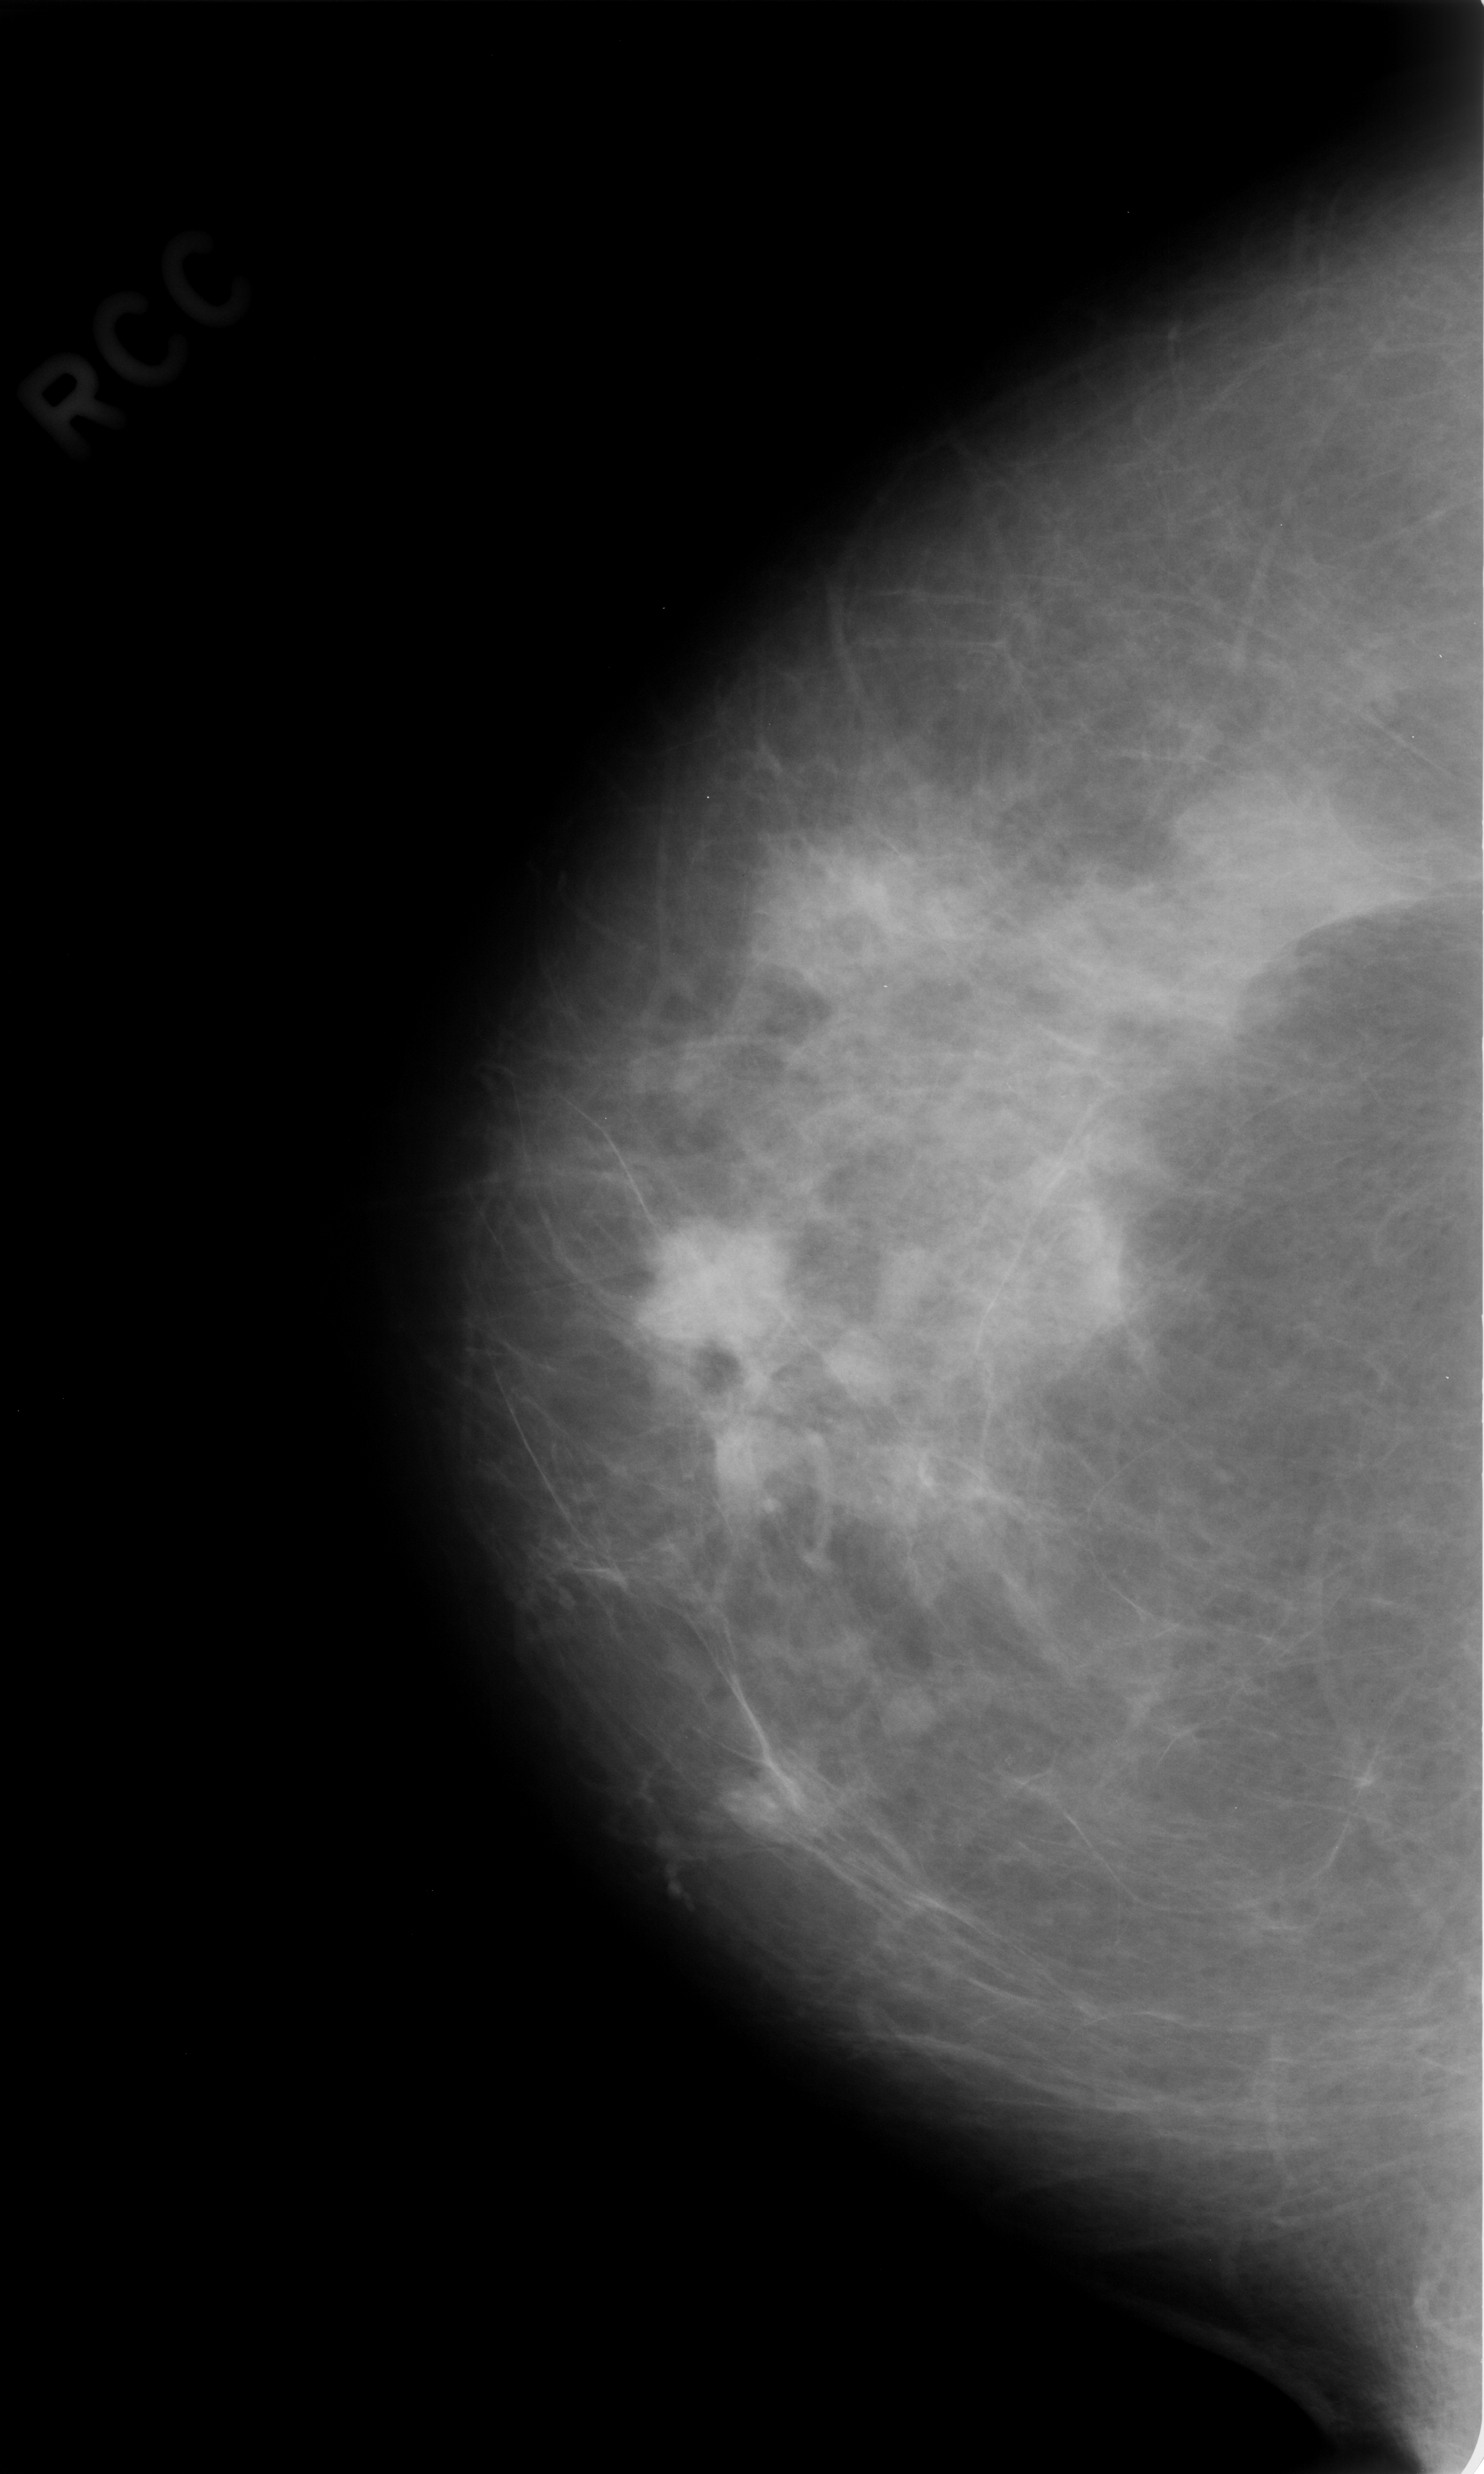
Digitized screen-film mammogram; right breast; craniocaudal (CC) view; BI-RADS breast density category 2 (scale 1–4).
Radiologist-marked abnormalities on this image: mass, shape lobulated, margins circumscribed; BI-RADS assessment category 4; subtlety rating 5 on a 1 (subtle) to 5 (obvious) scale; pathology (as recorded): benign.